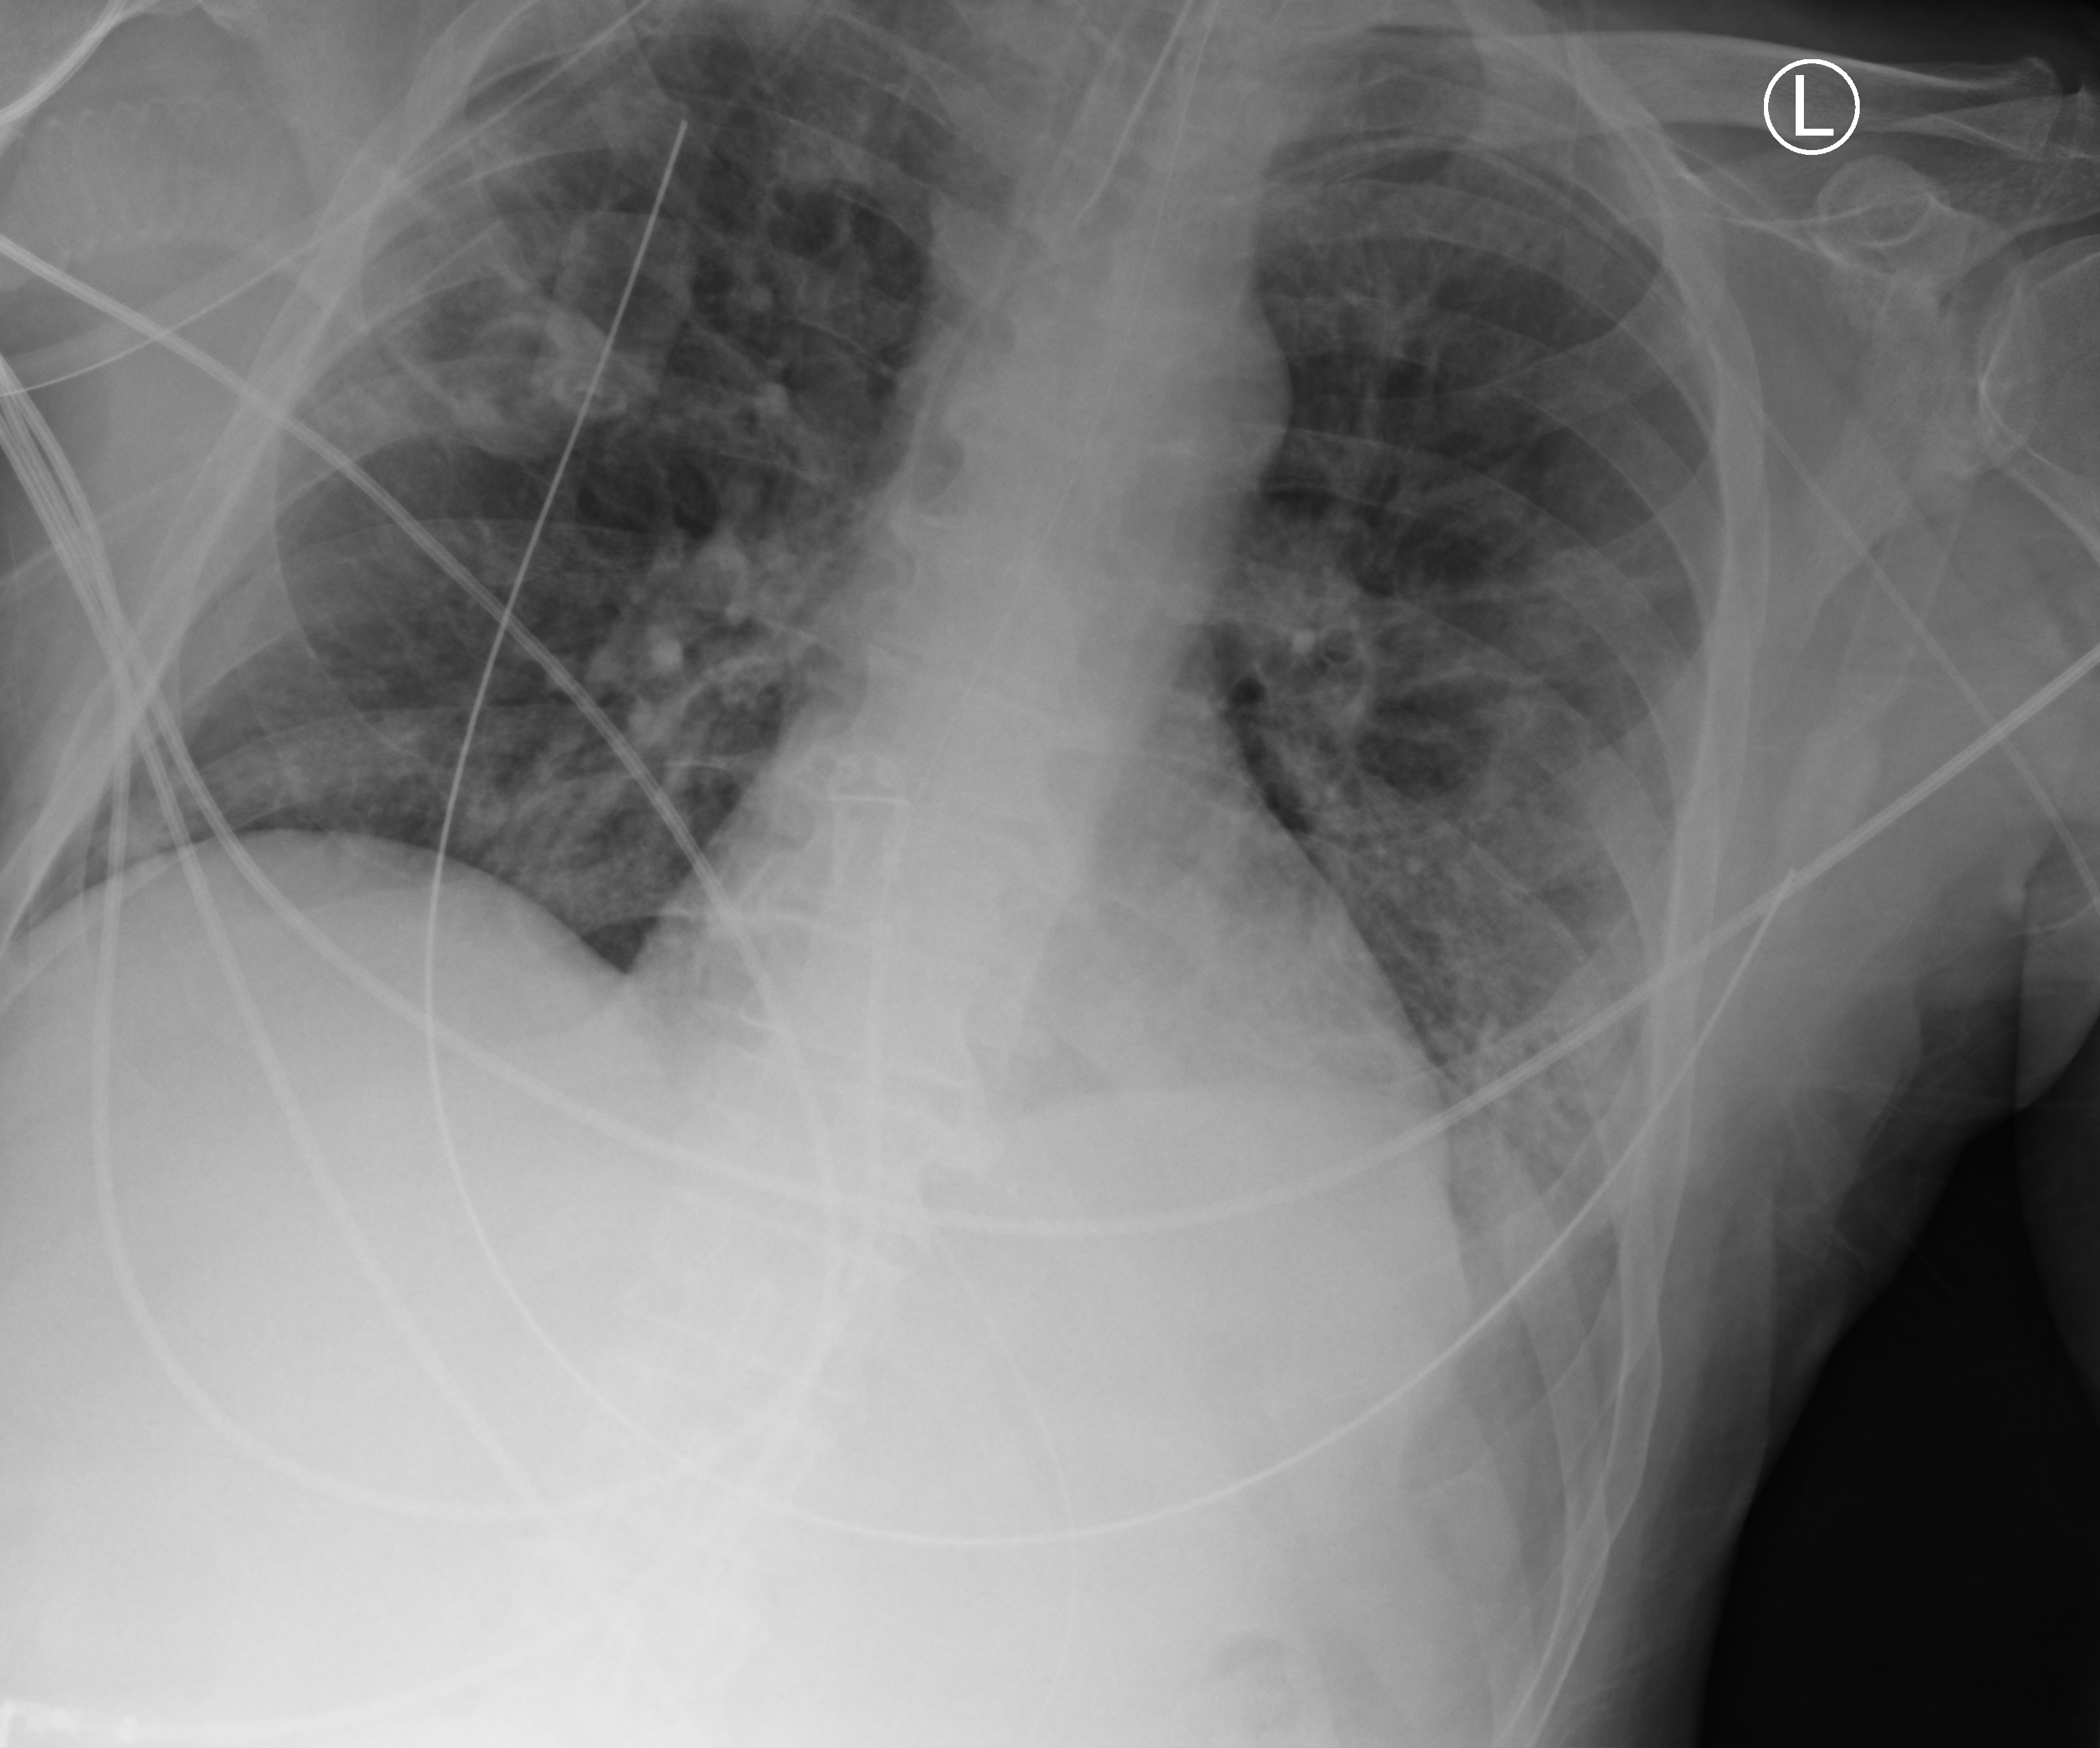
Chest X-ray (portable); anteroposterior (AP) projection. Patient hospitalised with COVID-19; male, aged 60–74 years.
Admission-level facts for this patient (not findings on this image; timing relative to this image not recorded): mechanically ventilated during this hospital stay: yes; admitted to intensive care during this hospital stay: yes; hypertension (admission record): yes.